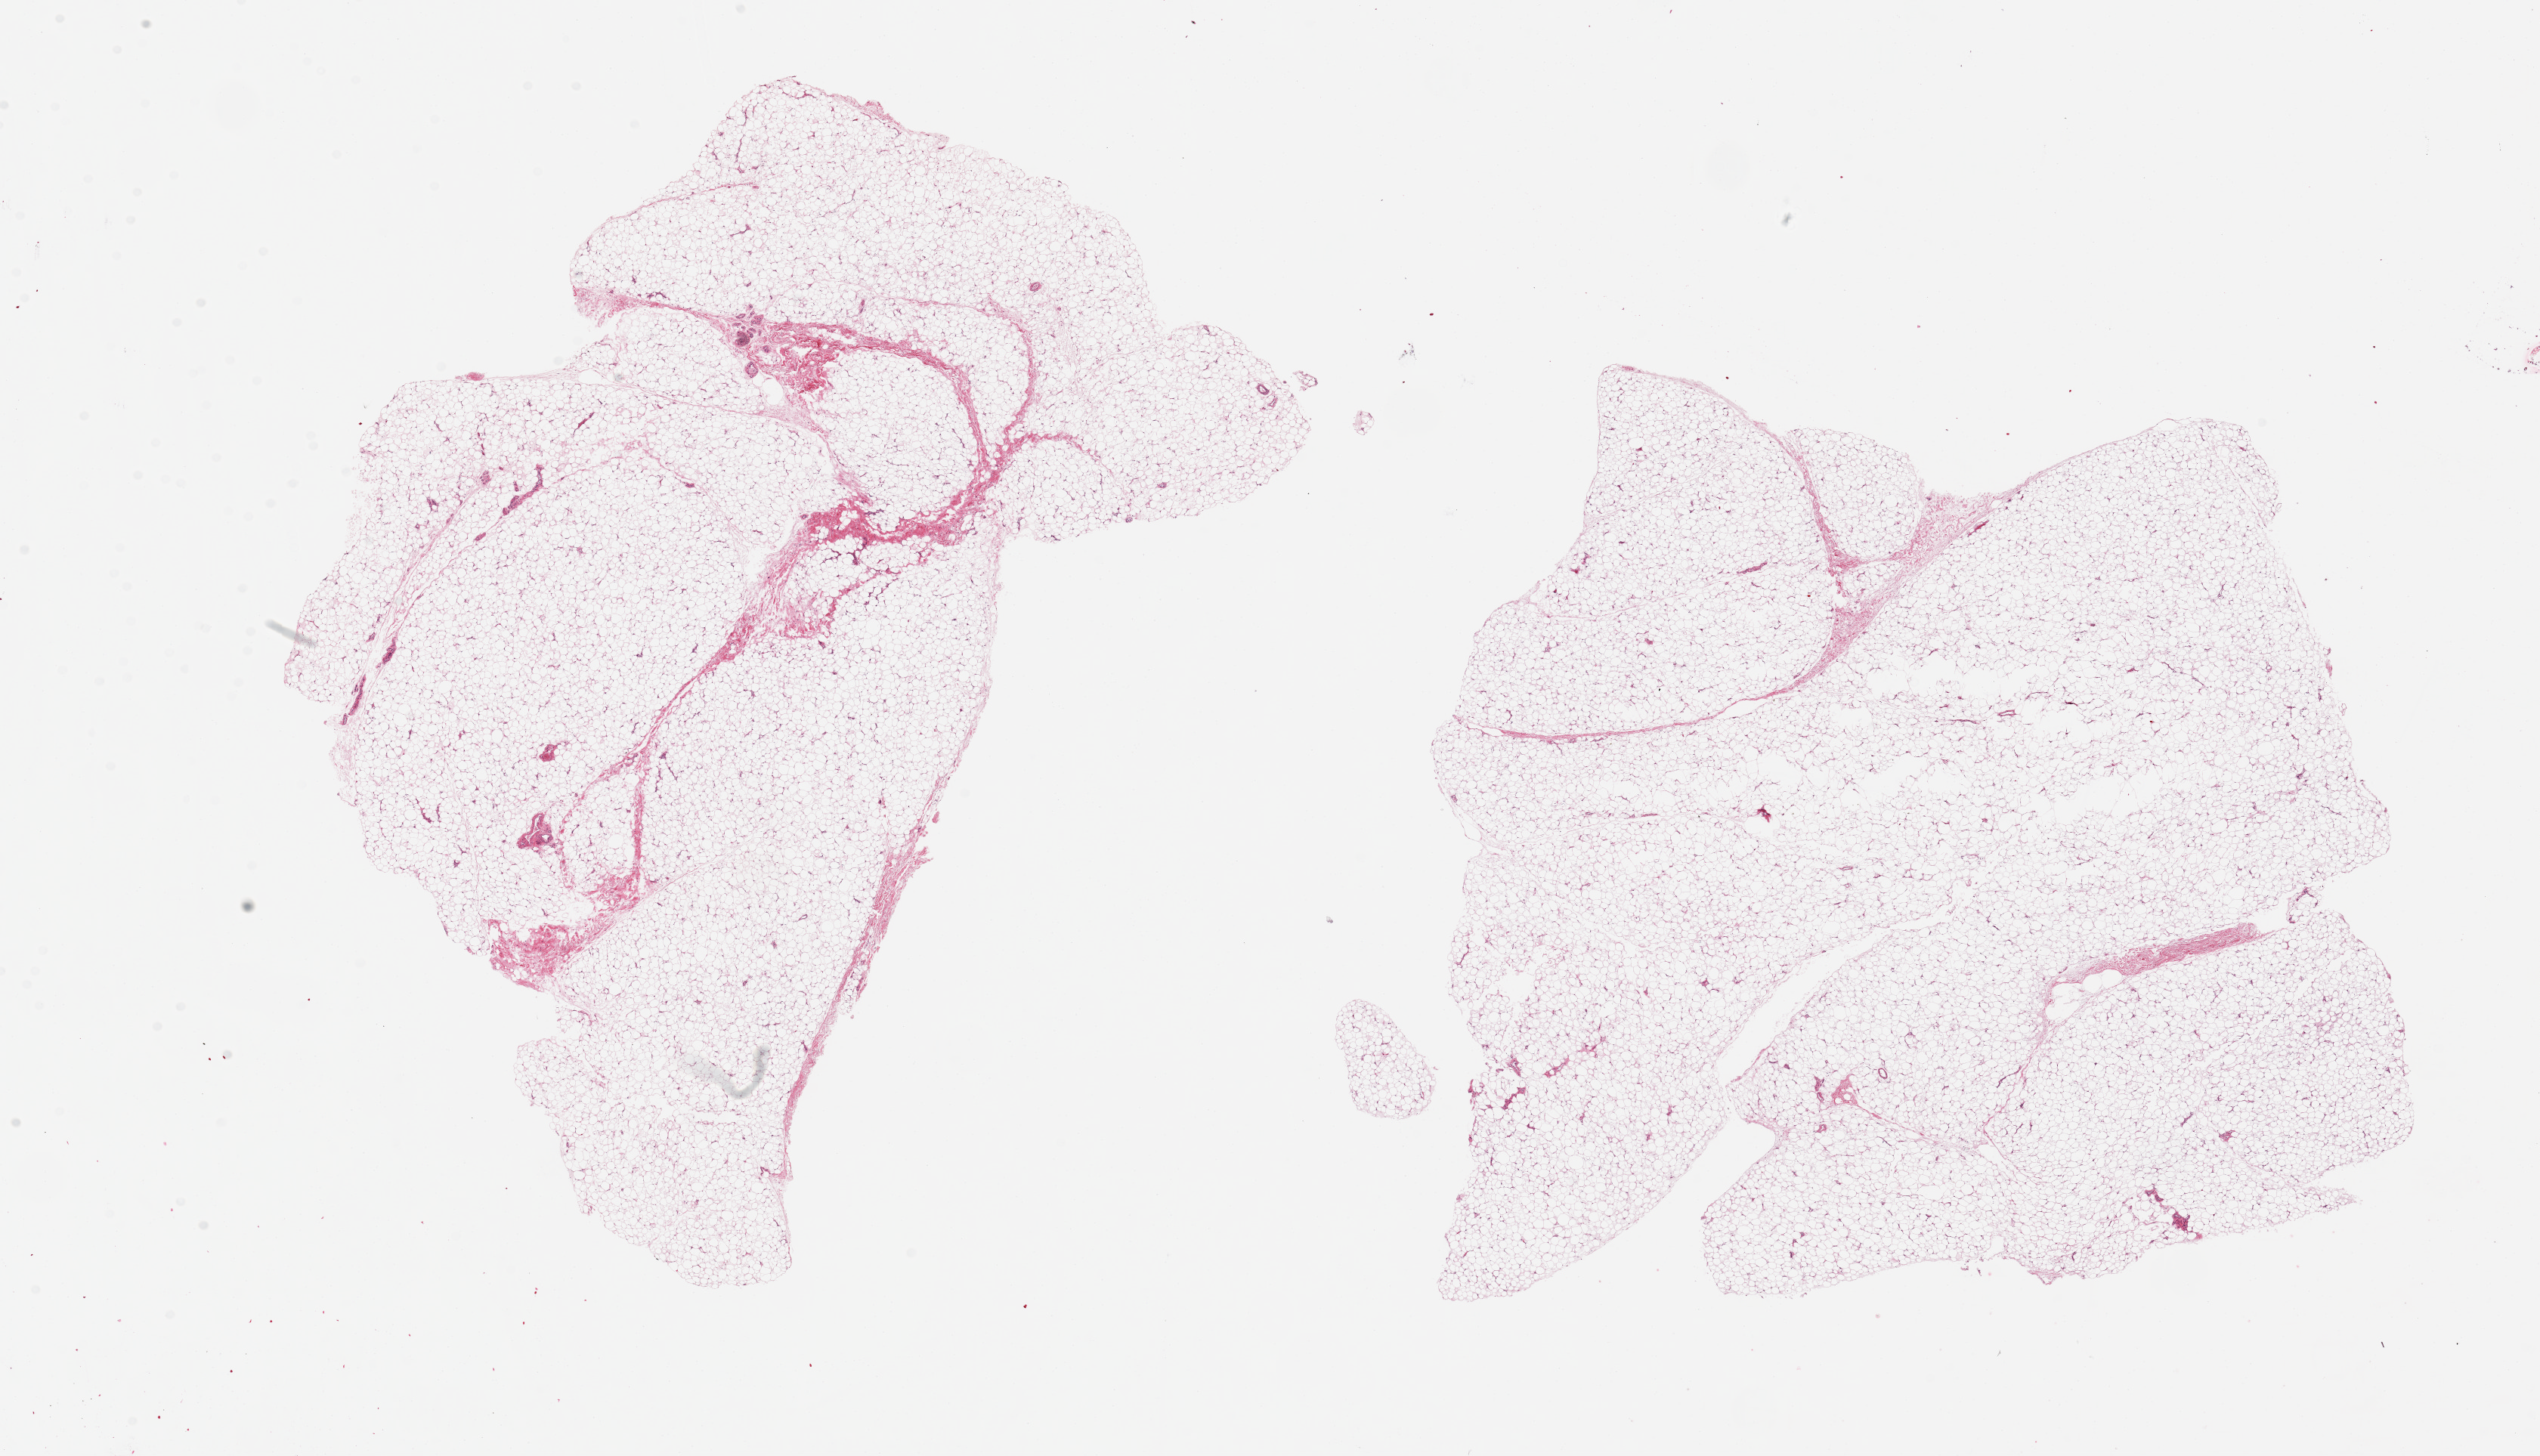
Hematoxylin and eosin (H&E) whole-slide image, brightfield — low-resolution overview of the scanned area, about 26.6 x 15.2 mm (slide scanned at 20x); PAXgene-fixed paraffin-embedded (PFPE) section; sampled site (target tissue): adipose tissue; donor tissue sample.
Reviewer comment on this tissue sample: 2 ~ 9x7mm aliquots, areas of poor/under-fixation centrally.